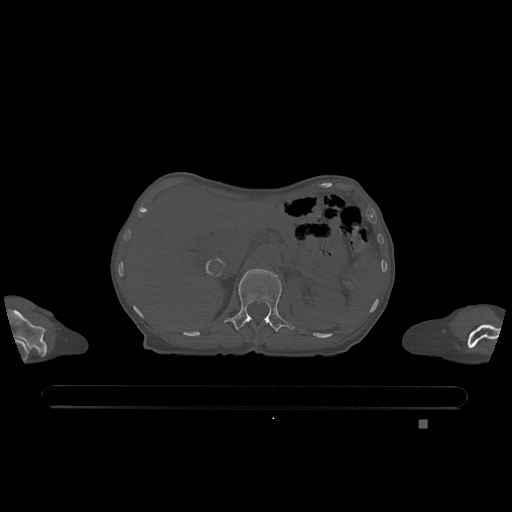
CT including the spine, one axial slice. Position 482 of 1317 along the scan axis. Bone window (W 1800 / L 400 HU). 0.5 mm slice thickness. 512 × 512 image matrix. Patient: female, 74 years. Case-level facts recorded for this patient, not image findings: primary cancer: lung.
Structures marked on this image (semi-automatically segmented with operator editing):
- L1 vertebra: bounding box (x1, y1, x2, y2) in pixels: (224, 269, 294, 332)